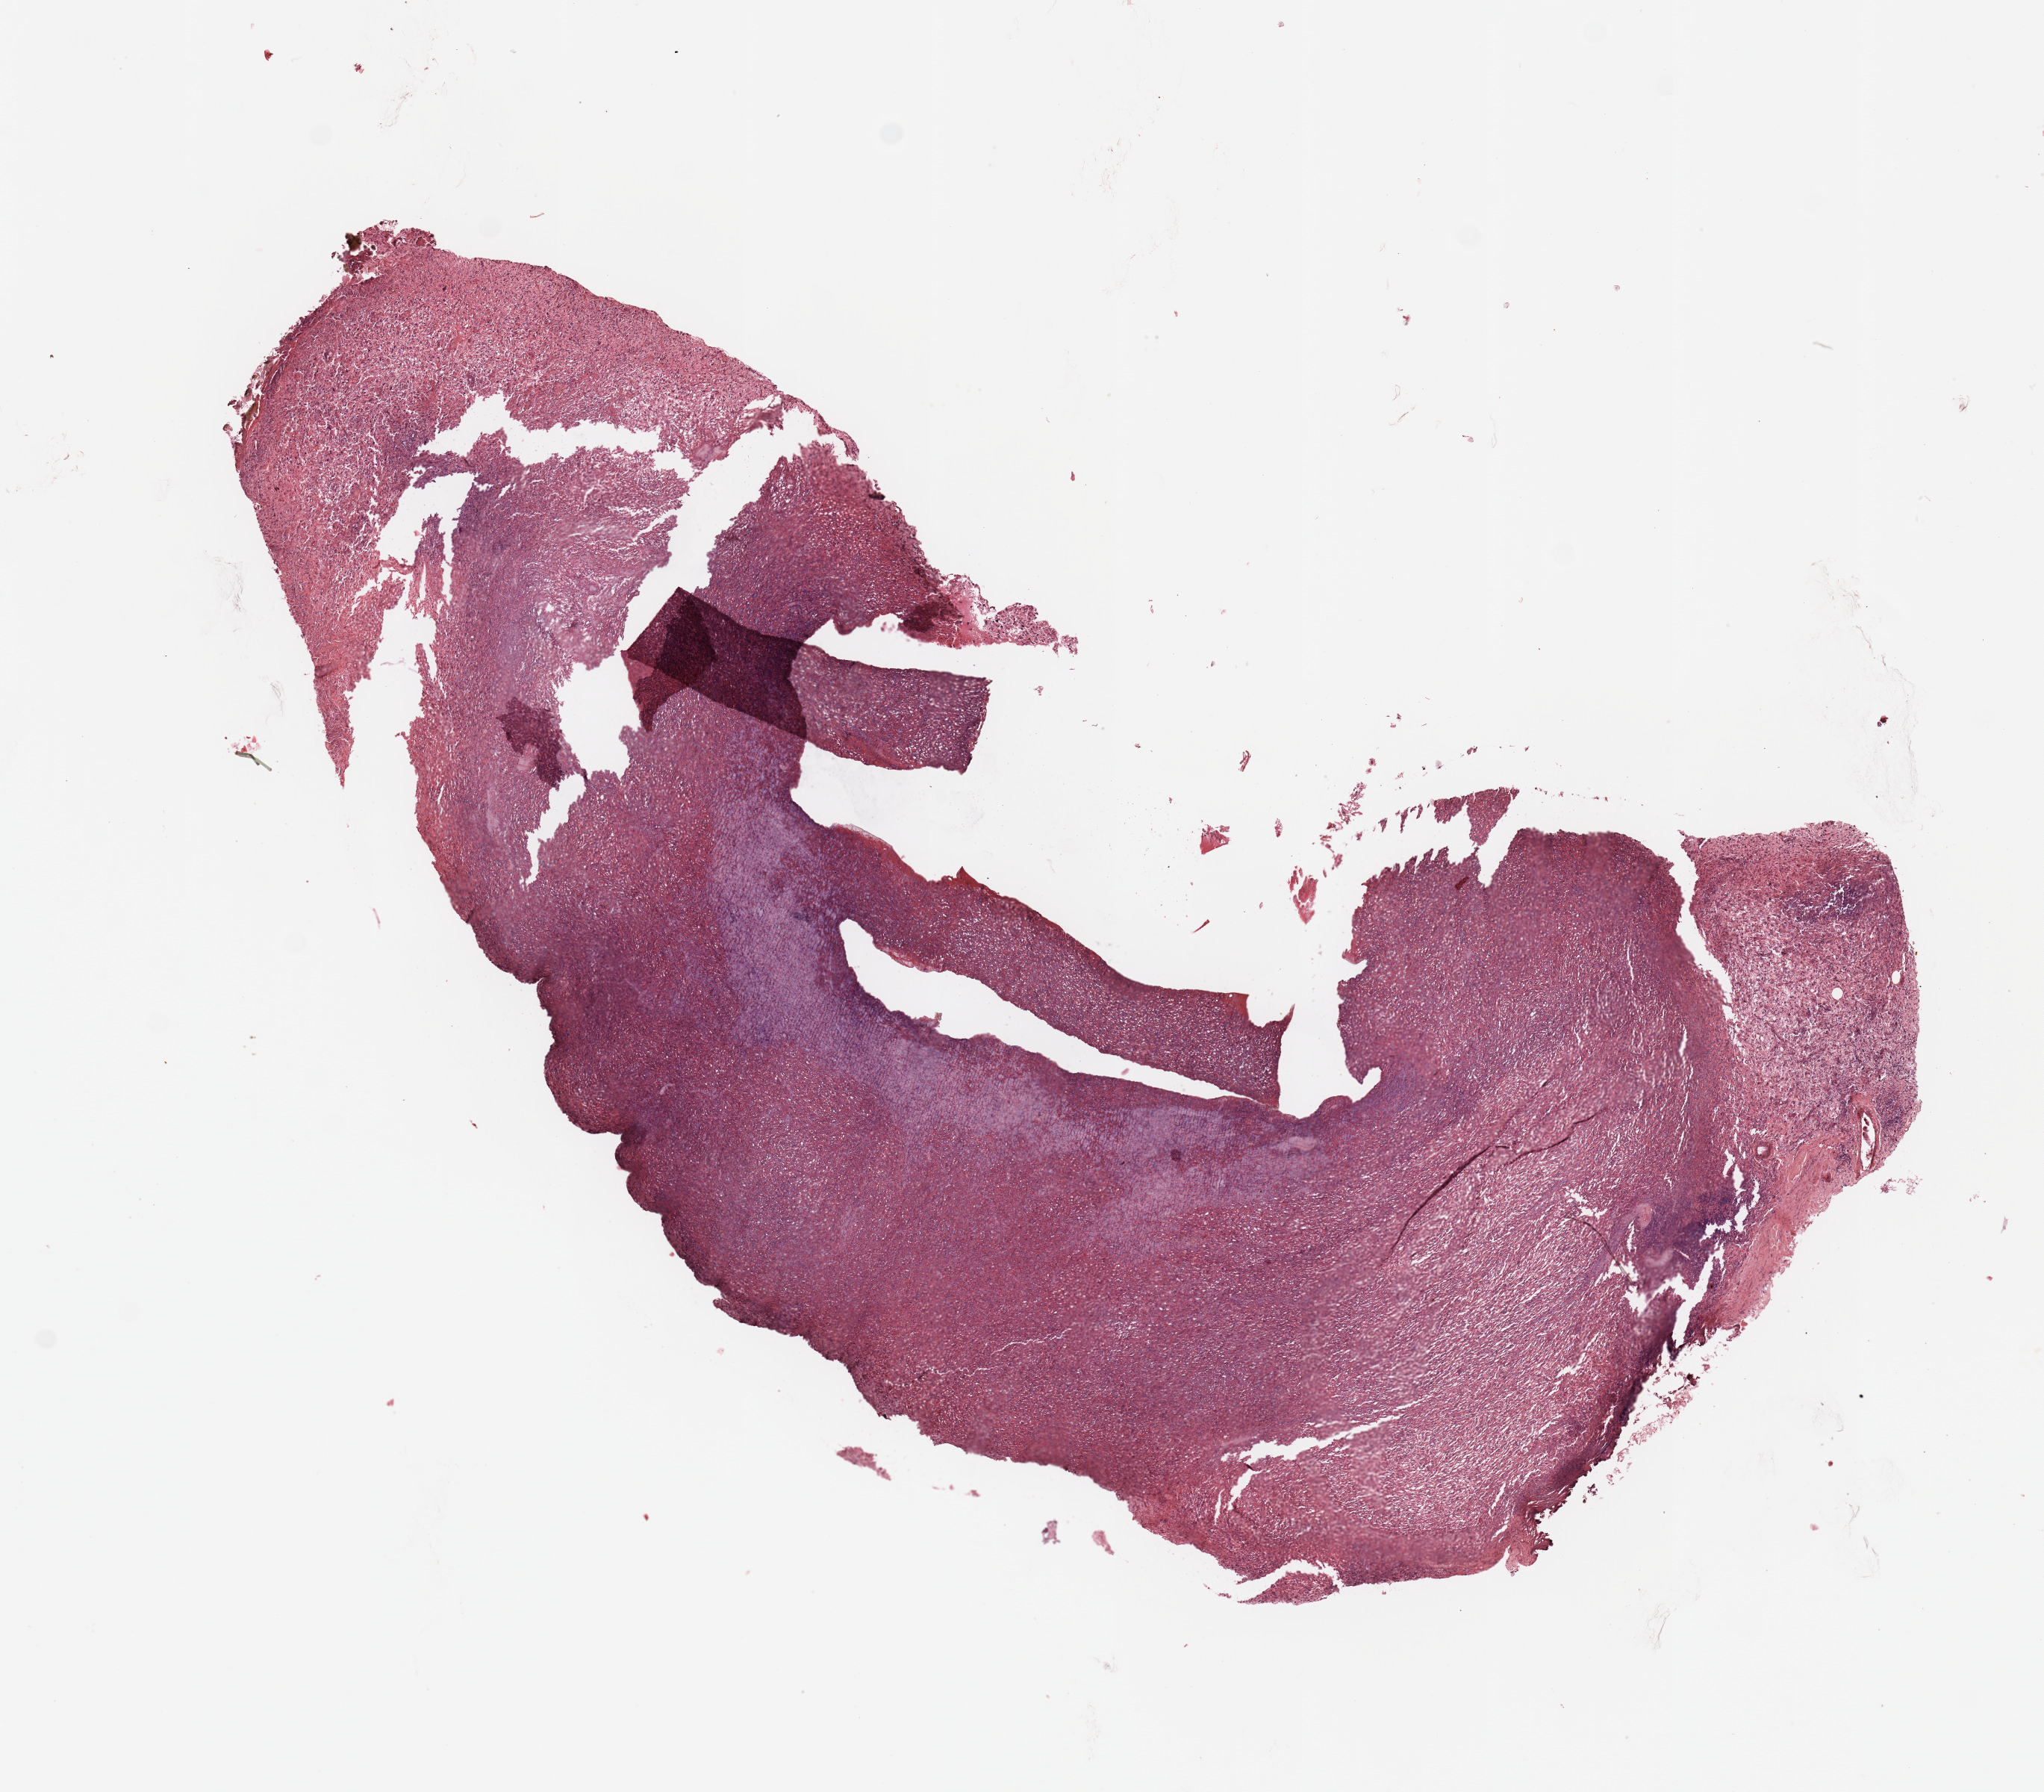
Digitized Hematoxylin and eosin (H&E) stained tissue section (whole slide) — a low-resolution overview of the entire scanned area, about 10.8 x 9.5 mm (acquisition: 20x scan). Tumour tissue sample. Patient: male, age 53 years.
Patient diagnosis (cohort enrolment): sarcoma (site not recorded at cohort level). Primary tumour site (as recorded): chest.